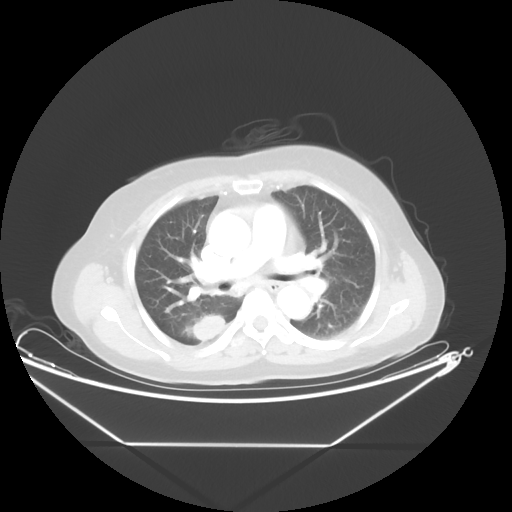
Chest CT, one axial slice. Slice 28 of 48 in the series (ordered by position). 100 kVp. Lung window (W 1500 / L -600 HU). 5 mm slice thickness. 512 × 512 image matrix. Female patient, age 62 years. From the clinical record (not read from this slice): clinical TNM (as recorded): T1c N0 M0.
Outlined on this slice (bounding box drawn by a radiologist):
- lung tumour (recorded histology: adenocarcinoma): bounding box [x1, y1, x2, y2] px = [185, 309, 228, 349]